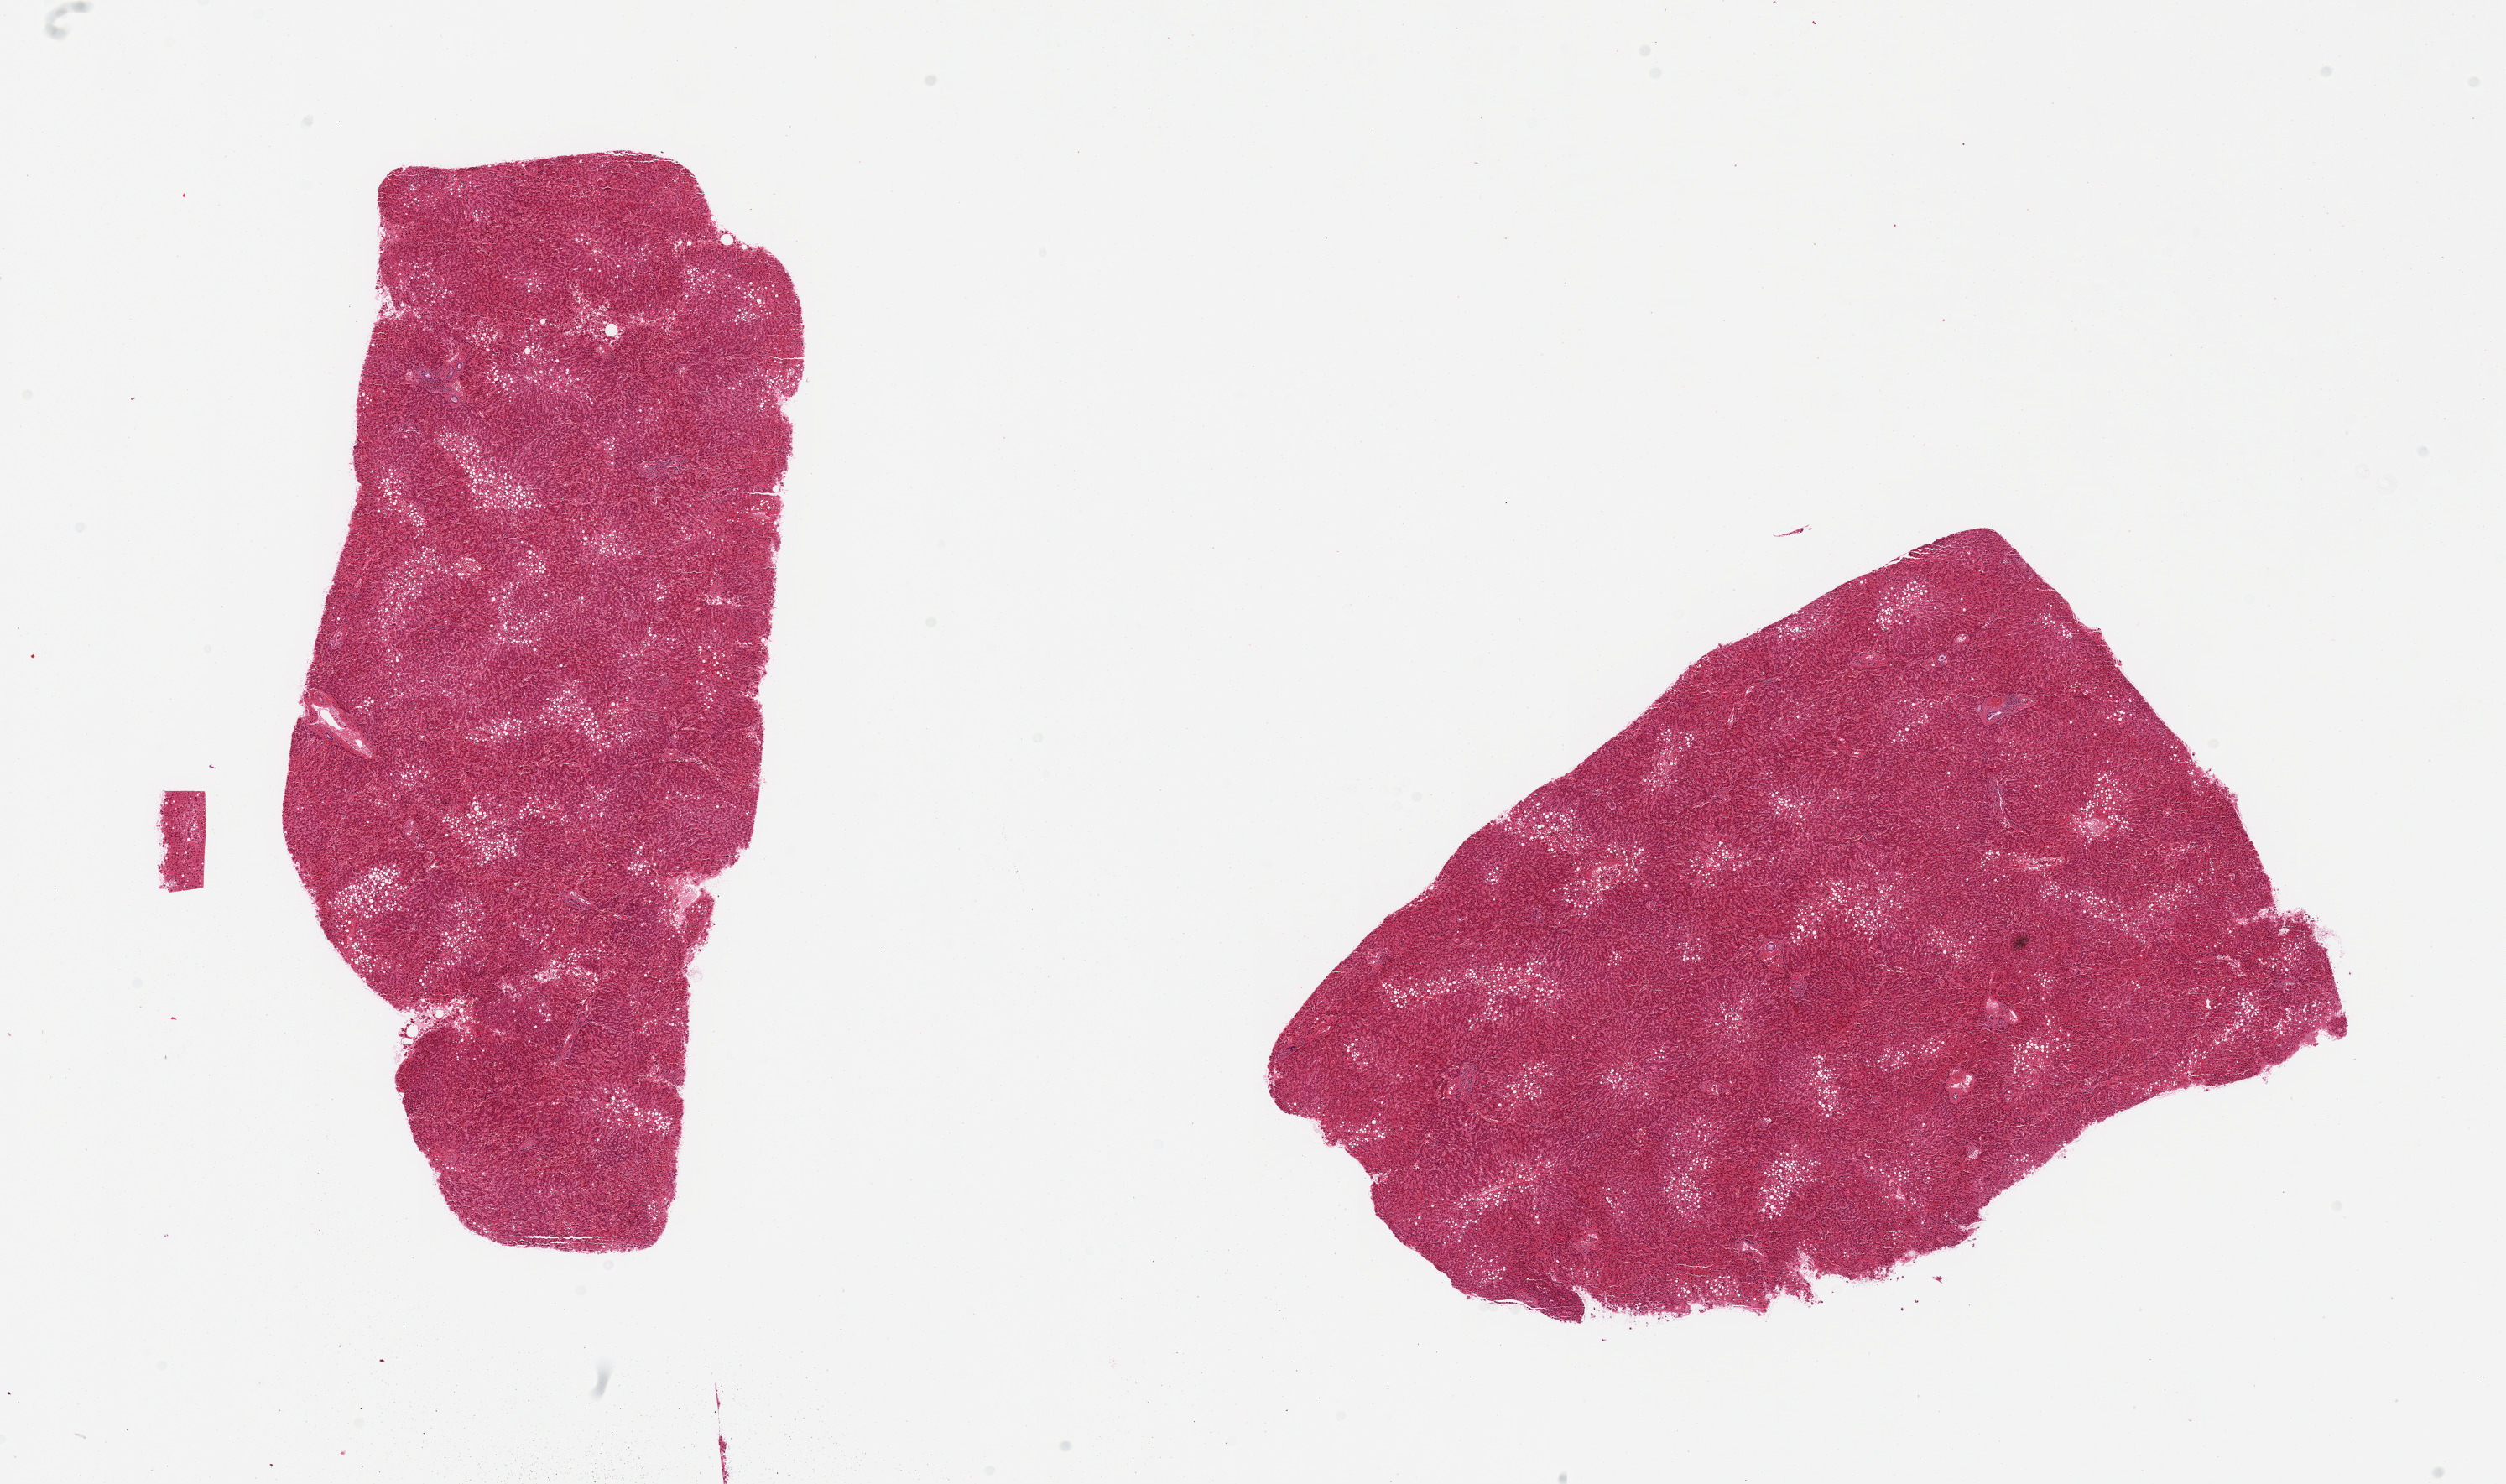
Digitized haematoxylin and eosin-stained section, brightfield — low-resolution overview of the scanned area, about 23.6 x 14.0 mm, PAXgene-fixed, paraffin-embedded tissue, target tissue: liver, tissue donor sample. Donor: female.
Review note (as recorded): 2 pieces, mild macrovesicular steatosis, passive congestion.